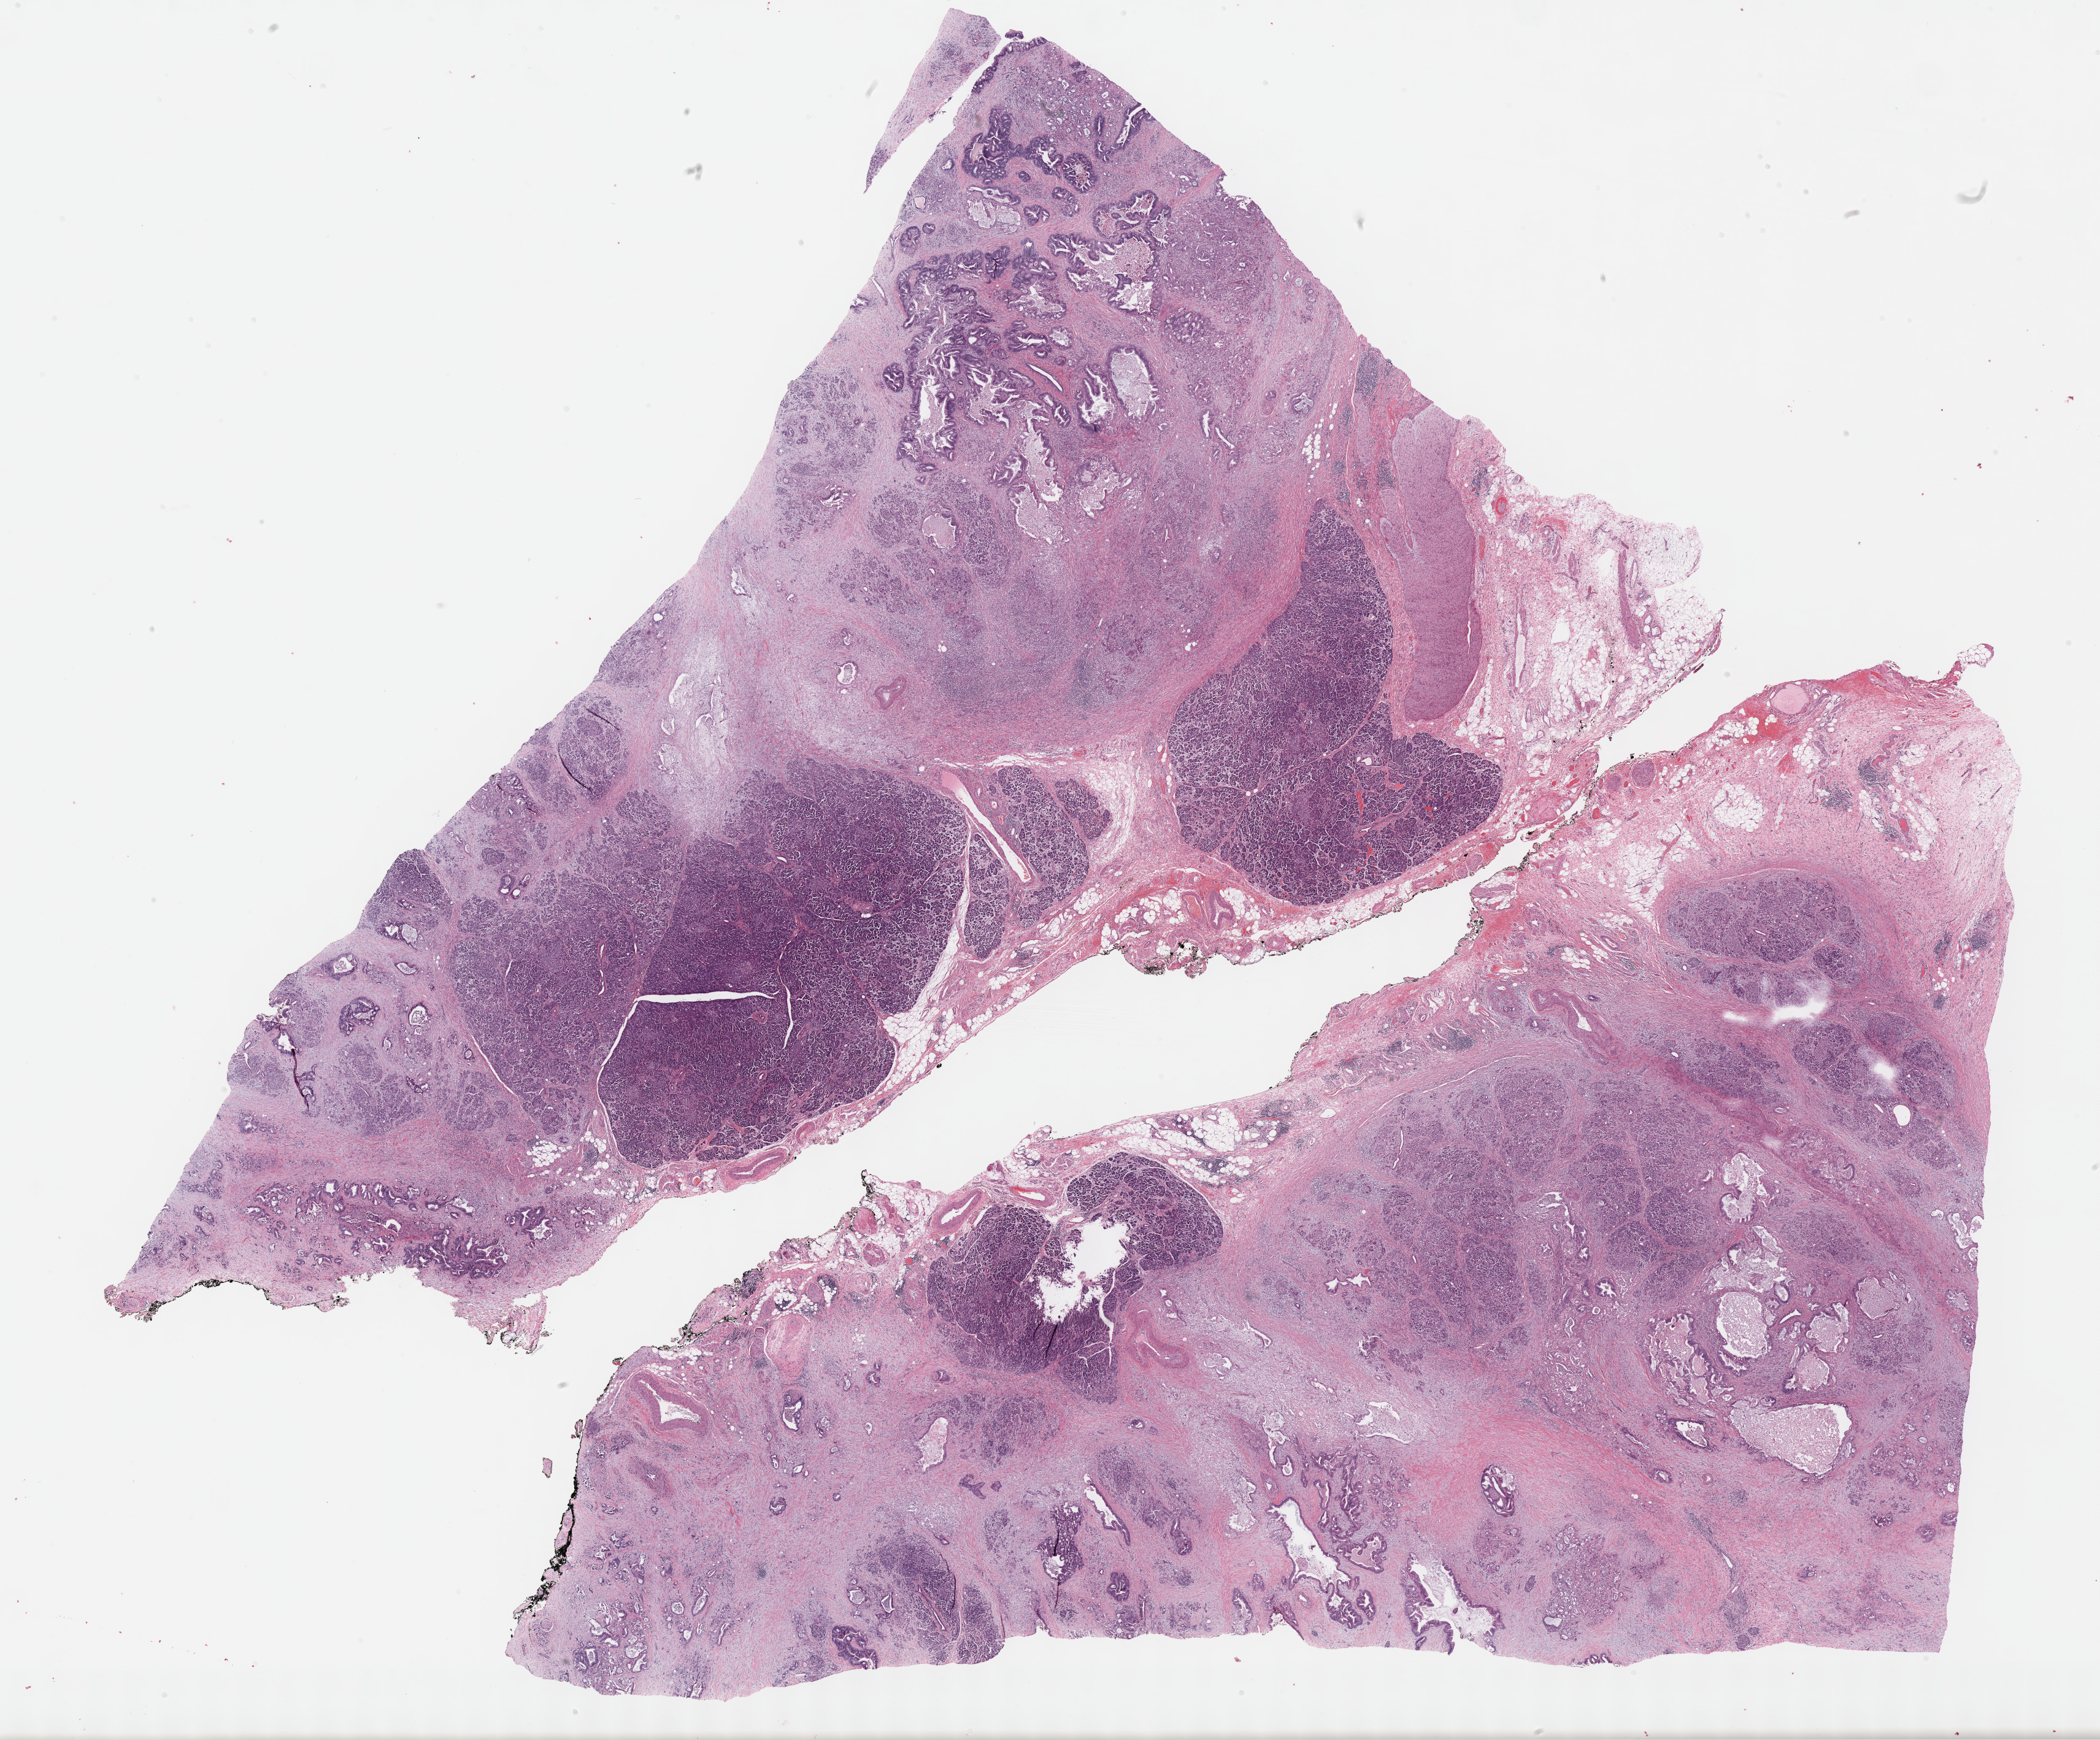
Whole-slide histology image, Hematoxylin and eosin (H&E) stained — a low-resolution overview of the entire scanned area, about 27.7 x 22.9 mm. Formalin-fixed paraffin-embedded (FFPE) diagnostic section. Sample: primary tumour, pancreas. Male patient; age at initial diagnosis 77 years. Histologic grade: G2 (moderately differentiated).
AJCC pathologic stage: IIA. Lymph nodes positive (case pathology): 0 of 14 examined. Histologic diagnosis: Infiltrating duct carcinoma, NOS (head of pancreas).